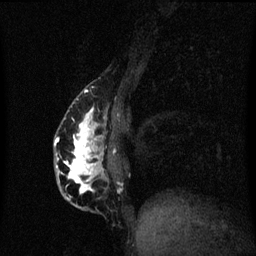
Breast MRI (dynamic contrast-enhanced), one sagittal slice; position 20 of 60 along the scan axis; dynamic contrast-enhanced series, image 2 of 3 at this slice position (ordered by acquisition); 1.5 T; TE 4.2 ms, TR 8.4 ms; 2 mm slice thickness; 256 × 256 image matrix, field of view 200 × 200 mm. Female patient, age 40 years.
Annotated regions visible in this slice (semi-automatic segmentation, software-assisted and operator-edited):
- analysis volume of interest (the breast-tissue region the enhancement analysis was run in; not a lesion): bounding box (x1, y1, x2, y2) in pixels: (55, 84, 115, 211)
- tumour enhancement mask (voxels above the 70 % enhancement threshold inside the analysis volume of interest): (55, 98, 105, 201)